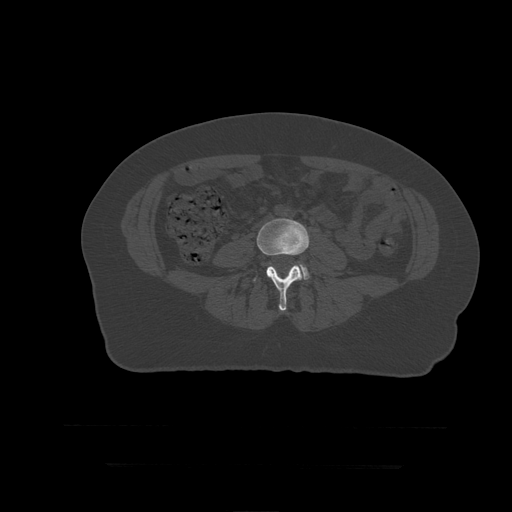
CT including the spine, one axial slice. Slice 91 of 399 in the series (ordered by position). Bone window (W 1800 / L 400 HU). 1.25 mm slice thickness. 512 × 512 image matrix. Patient age 41 years. From the clinical record (not read from this slice): primary cancer: breast.
Annotated regions visible in this slice (semi-automatically segmented with operator editing):
- L4 vertebra: box from (x=253, y=218) to (x=310, y=312) px
- L5 vertebra: (x=298, y=262)–(x=310, y=280)